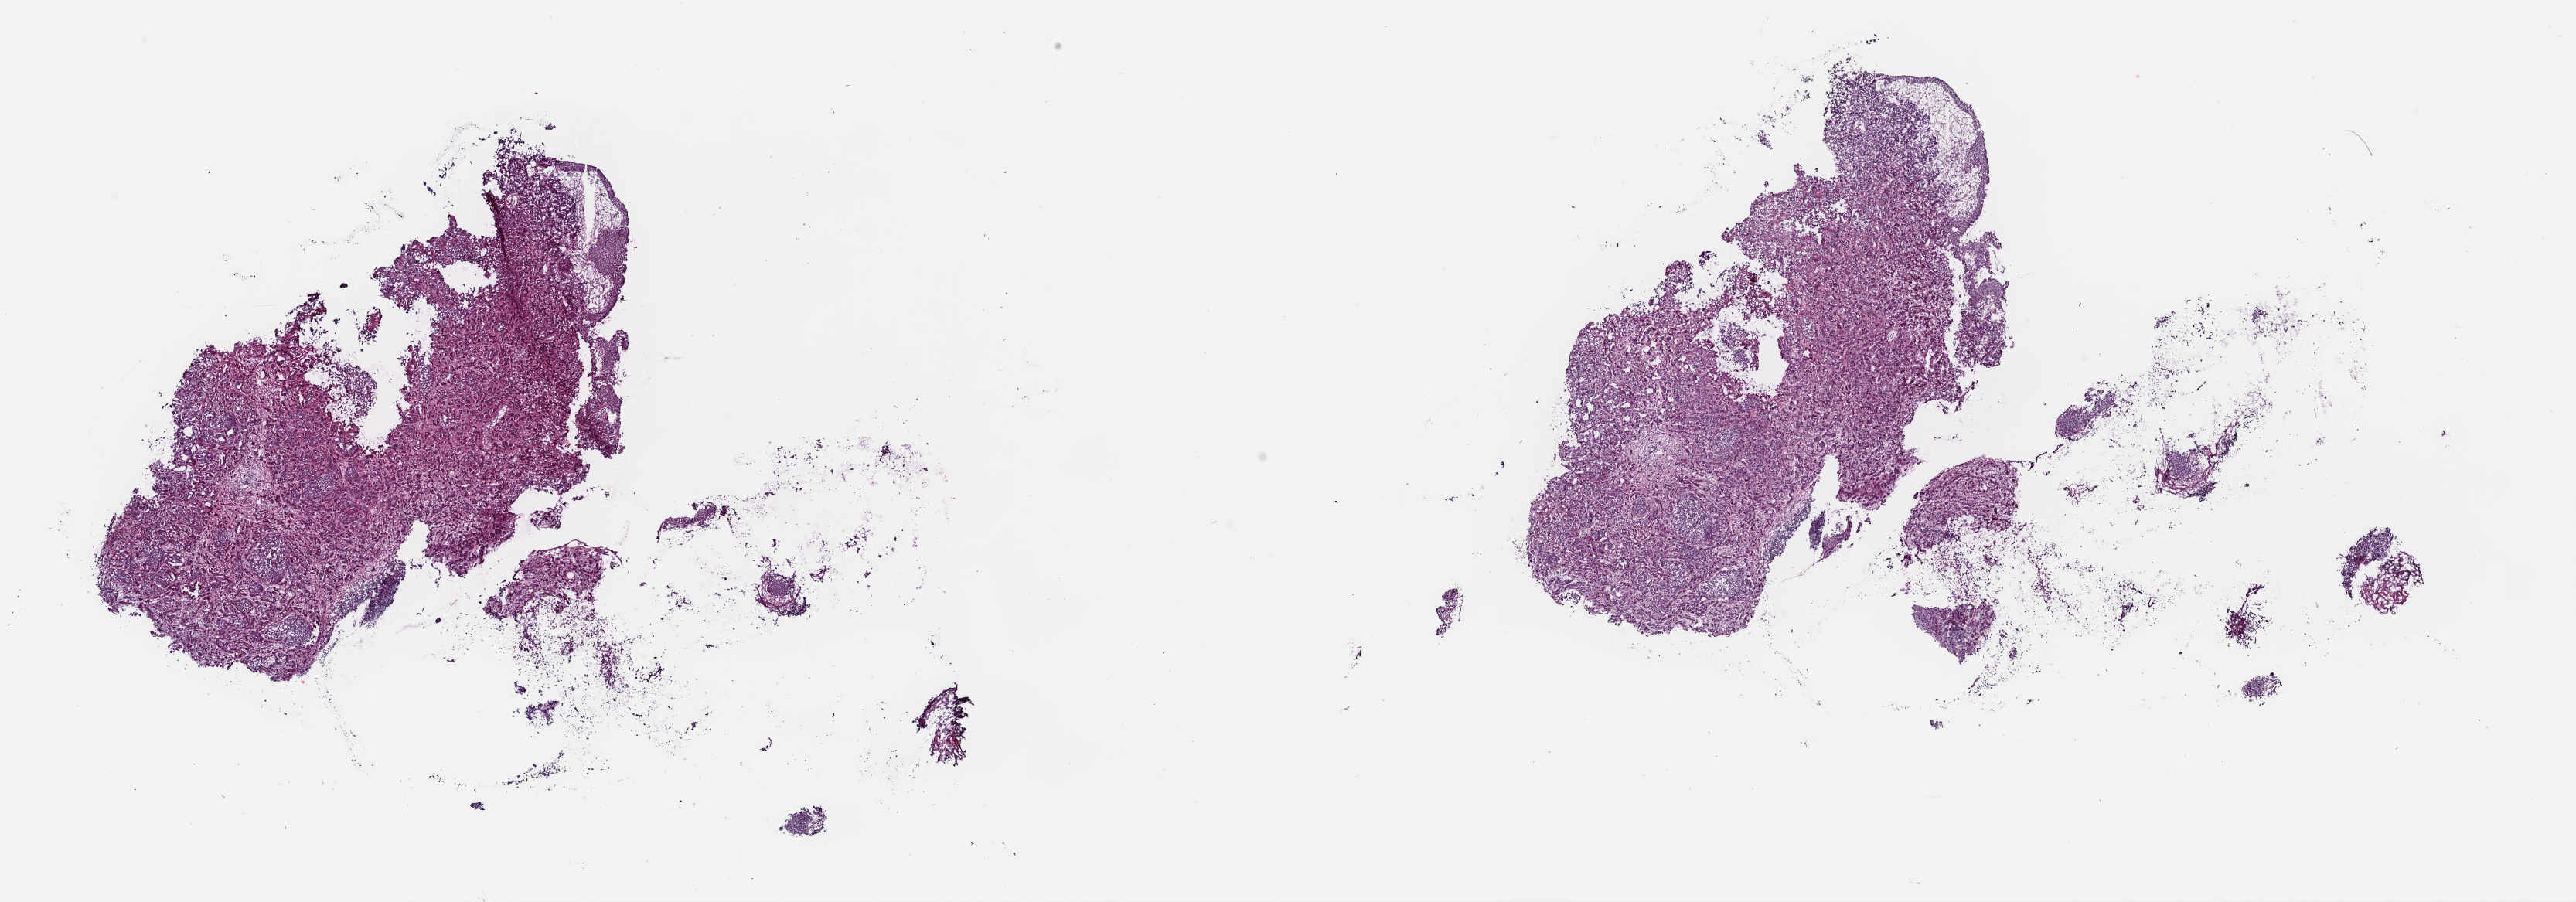
Whole-slide histology image, H&E-stained — low-resolution overview of the scanned area, about 26.3 x 9.2 mm (from a 40x scan); frozen section from the top of the tissue portion; sample: primary tumour, bladder. Female, age 80 years at initial diagnosis. Histologic grade: high grade. Composition of this section per pathologist review: tumour cells 100%, tumour nuclei 90%, normal cells 0%, stromal cells 0%, necrosis 0%. Infiltration values recorded for this section: lymphocyte infiltration 1%, monocyte infiltration 0%, neutrophil infiltration 0%.
• AJCC pathologic stage: III (7th edition)
• diagnosis: Transitional cell carcinoma (bladder neck)